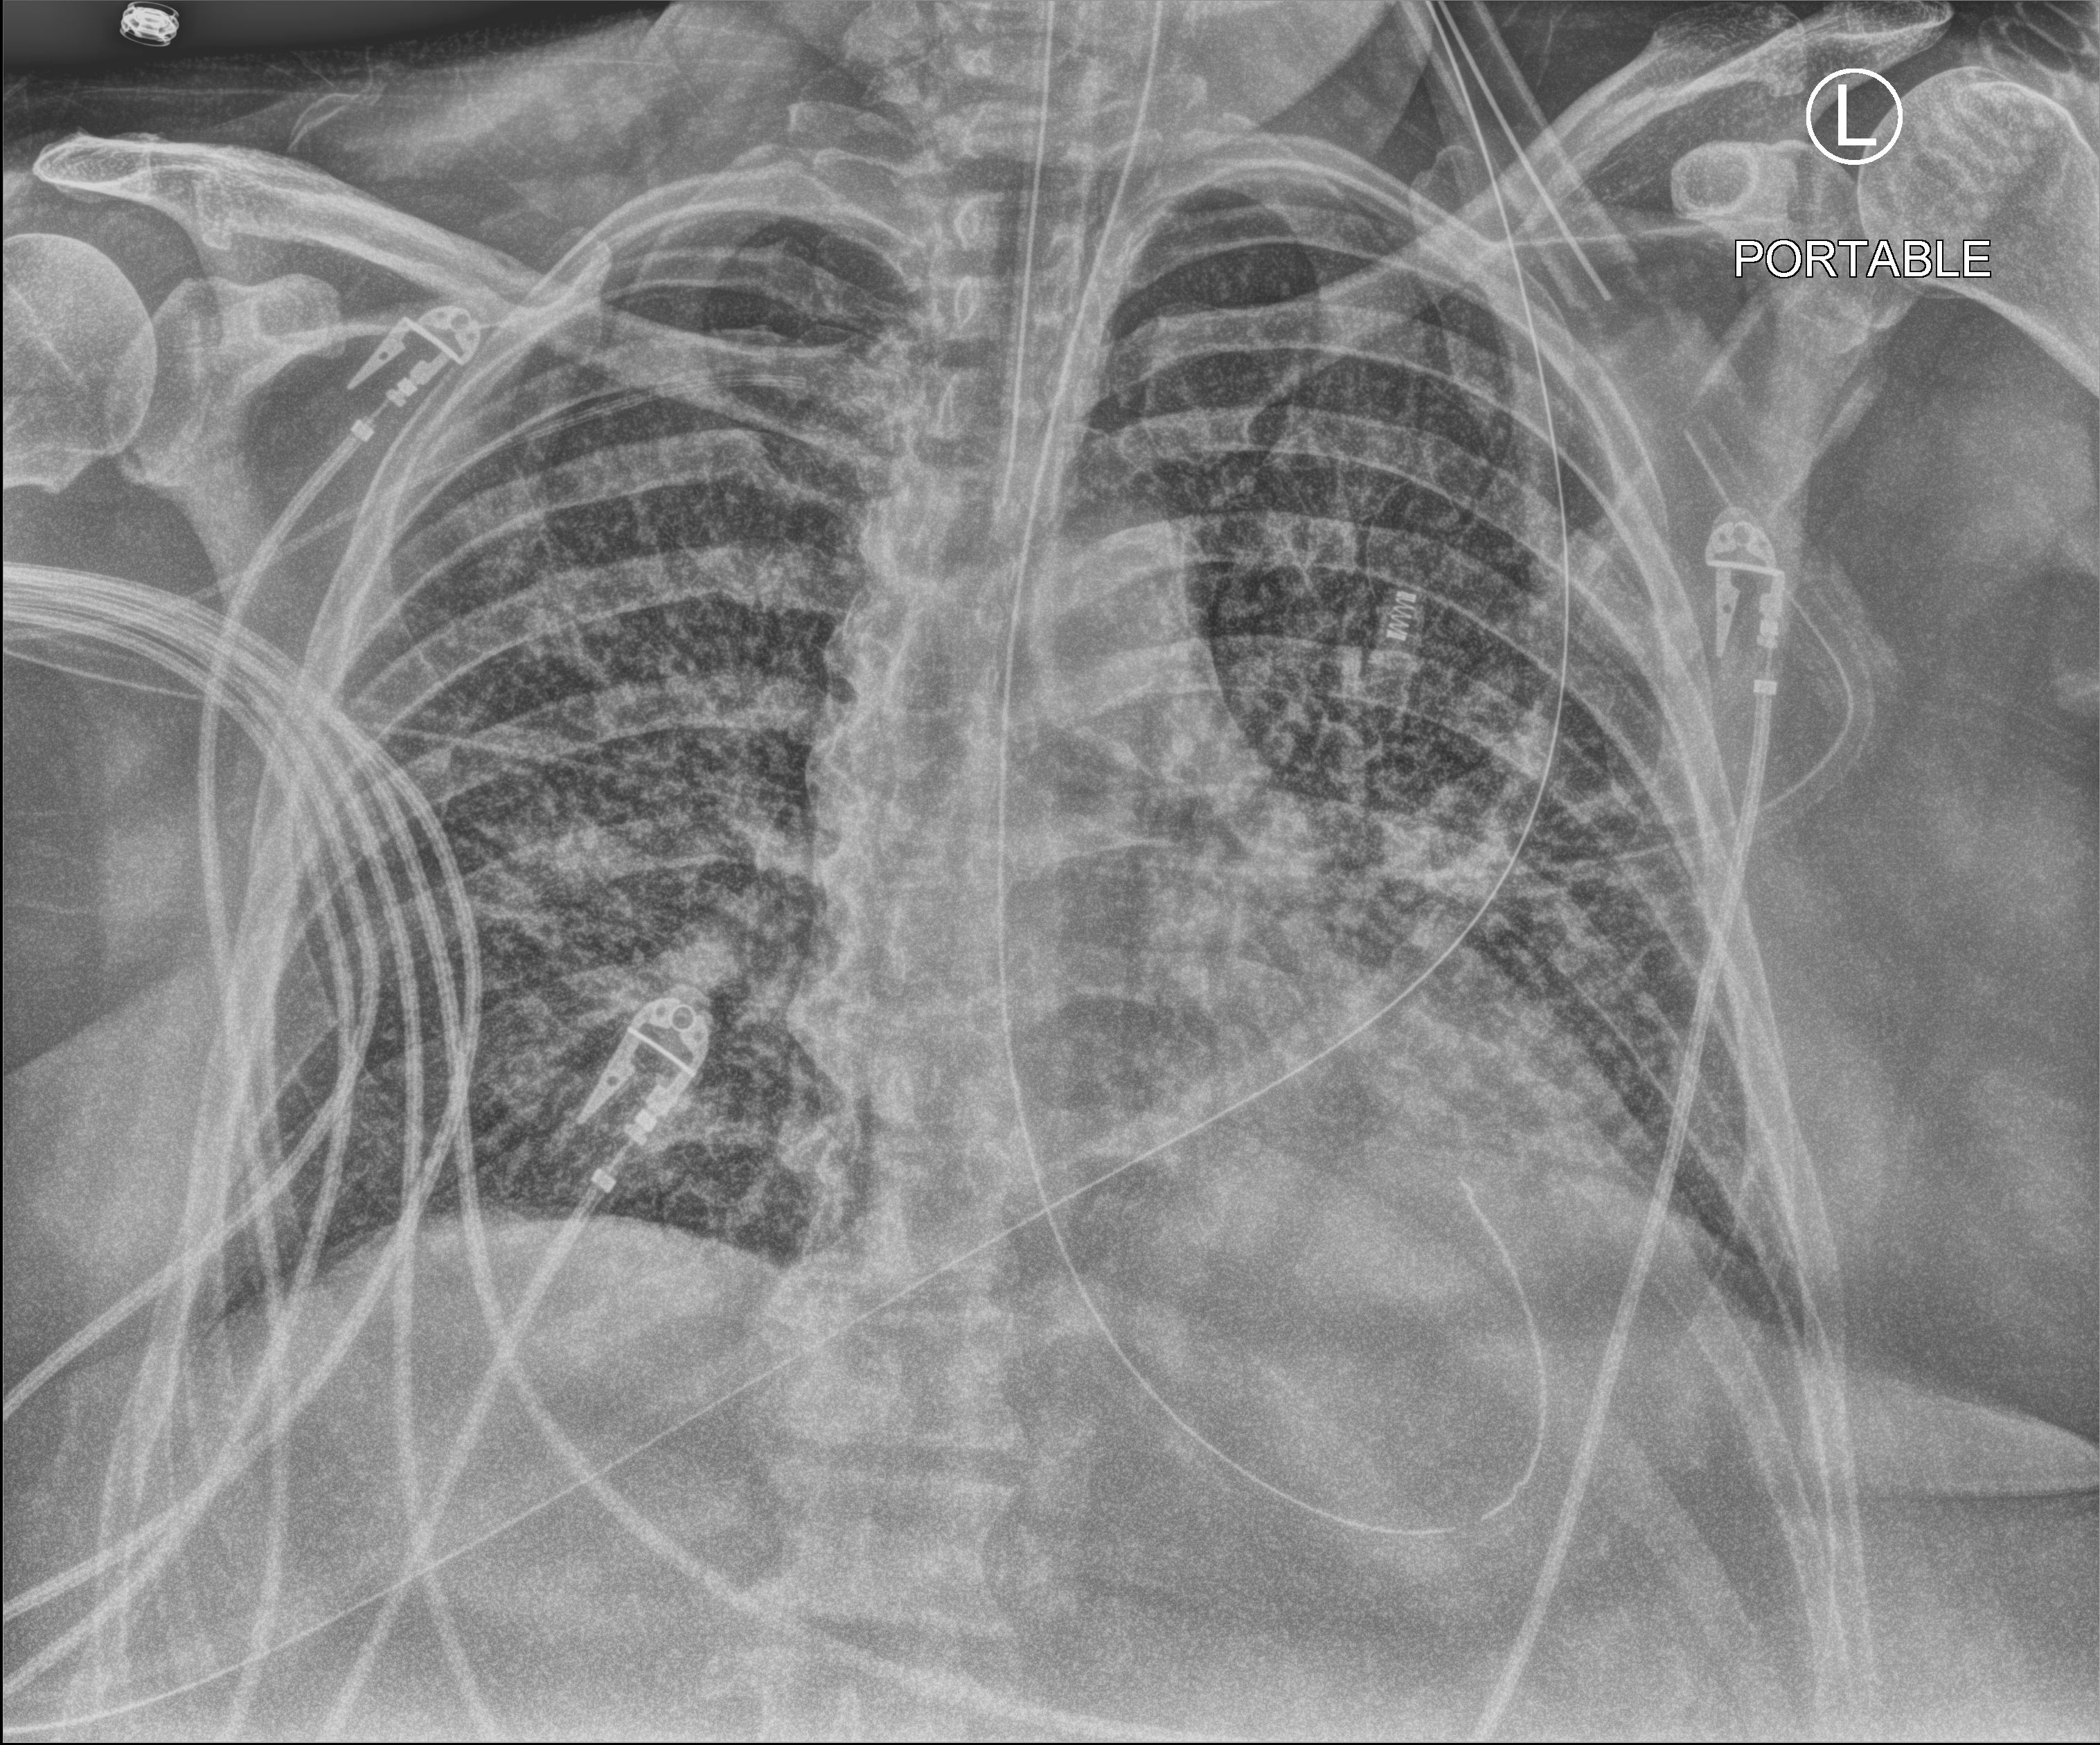
Portable chest radiograph, anteroposterior (AP) projection. Patient hospitalised with COVID-19, aged 18–59 years.
Admission-level facts for this patient (not findings on this image; timing relative to this image not recorded): length of hospital stay: 28 days; admitted to intensive care during this hospital stay: yes.